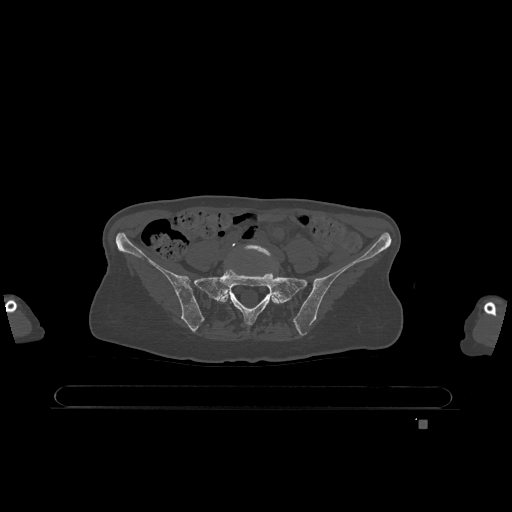
CT including the spine, one axial slice. Slice 205 of 1317 in the series (ordered by position). Bone window (W 1800 / L 400 HU). 512 × 512 image matrix. Female patient, age 74 years. Case-level facts recorded for this patient, not image findings: primary cancer: lung.
Annotated regions visible in this slice (semi-automatically segmented with operator editing):
- L5 vertebra: bounding box (x1, y1, x2, y2) in pixels: (219, 244, 279, 304)